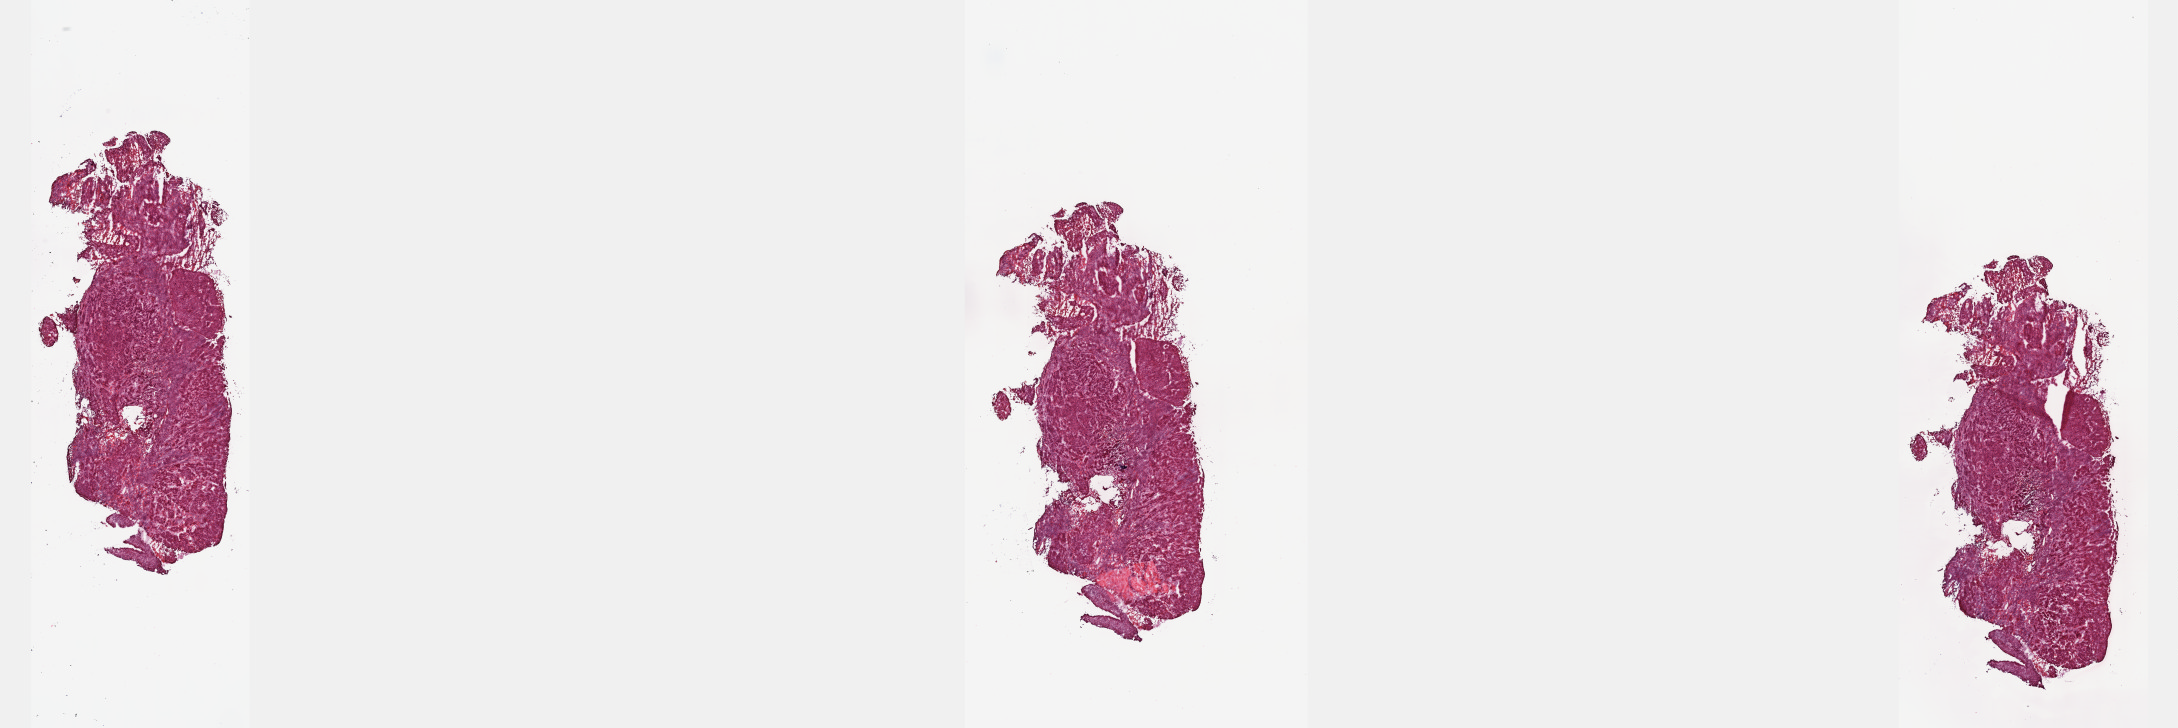
Digitized H&E-stained tissue section (whole slide) — a low-resolution overview of the entire scanned area, about 35.2 x 11.8 mm (acquisition: 40x scan), frozen section from the top of the tissue portion, cervix, primary tumour sample. Patient: female, age at initial diagnosis 42 years. Histologic grade: G3 (poorly differentiated). Slide review estimates, as recorded: tumour cells 80%, tumour nuclei 95%, normal cells 0%, stromal cells 15%, necrosis 5%. Inflammatory infiltration, as recorded: lymphocyte infiltration 0%, monocyte infiltration 0%, neutrophil infiltration 0%.
Histologic diagnosis: Squamous cell carcinoma, large cell, nonkeratinizing, NOS (cervix uteri). Lymph nodes positive (case pathology): 0 of 24 examined. FIGO stage: IB1.